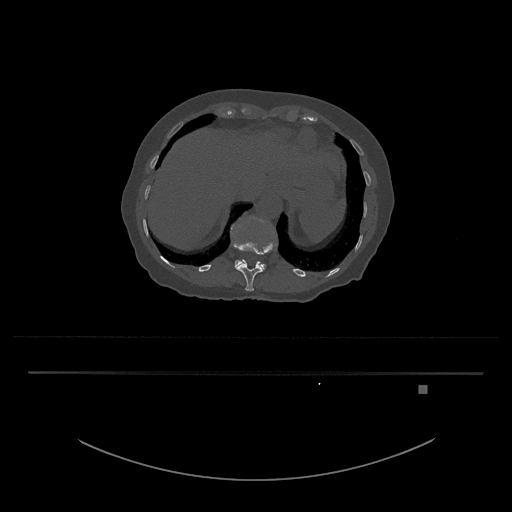
CT including the spine, one axial slice. Slice 594 of 797 in the series (ordered by position). Reconstruction kernel Br40s/3. 120 kVp. Bone window (W 1800 / L 400 HU). 0.5 mm slice thickness. 512 × 512 image matrix. Patient: female, 57 years. From the clinical record (not read from this slice): primary cancer: cervical.
Outlined on this slice (semi-automatically segmented with operator editing):
- L1 vertebra: bounding box <234,260,266,270> (left, top, right, bottom; pixels)
- T12 vertebra: <232,235,272,291>